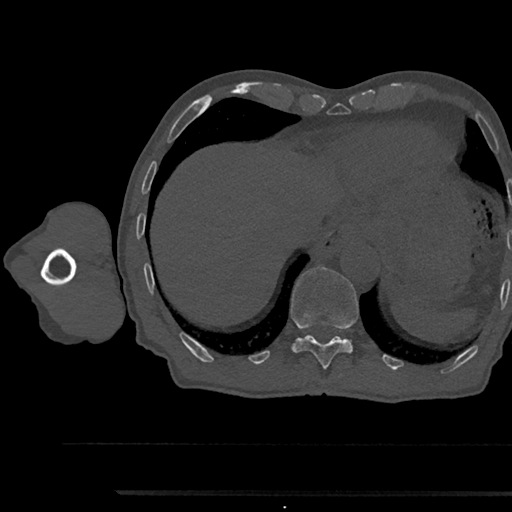
CT including the spine, one axial slice. 120 kVp. Bone window (W 1800 / L 400 HU). 0.5 mm slice thickness. 512 × 512 image matrix, field of view 367 × 367 mm. Male patient, age 79 years. Case-level facts recorded for this patient, not image findings: primary cancer: prostate.
Annotated regions visible in this slice (semi-automatically segmented with operator editing):
- T11 vertebra: bounding box (x1, y1, x2, y2) in pixels: (291, 266, 359, 370)